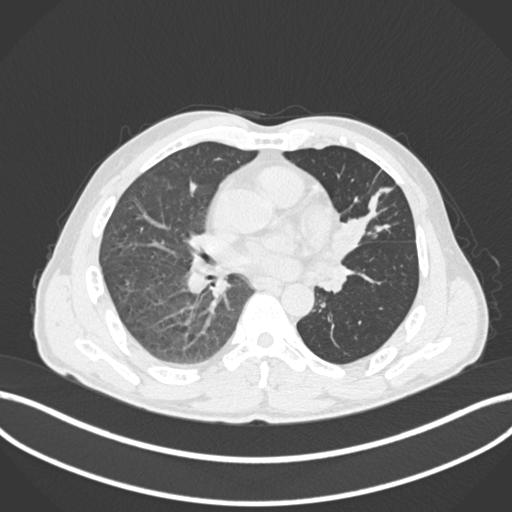
Chest CT, one axial slice; position 89 of 255 along the scan axis; 120 kVp; lung window (W 1500 / L -600 HU); 1 mm slice thickness; 512 × 512 image matrix, field of view 400 × 400 mm. Male patient, age 57 years. From the clinical record (not read from this slice): clinical TNM (as recorded): T2b N0 M0.
Annotated regions visible in this slice (rectangle marked by the reading radiologist):
- lung tumour (recorded histology: squamous cell carcinoma): bounding box <335,208,366,265> (left, top, right, bottom; pixels)